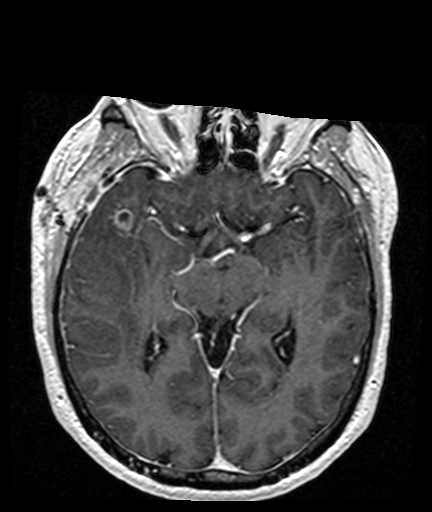
Brain MRI from a brain-tumour surgery series, one axial slice. Slice 96 of 176 in the series (ordered by position). T1-weighted post-contrast. 1 mm slice thickness. 432 × 512 image matrix, field of view 194 × 230 mm. From the clinical record (not read from this slice): histopathology: Glioblastoma; WHO grade: 4.
Outlined on this slice (expert manual segmentation):
- tumour: bounding box [x1, y1, x2, y2] px = [113, 210, 134, 247]